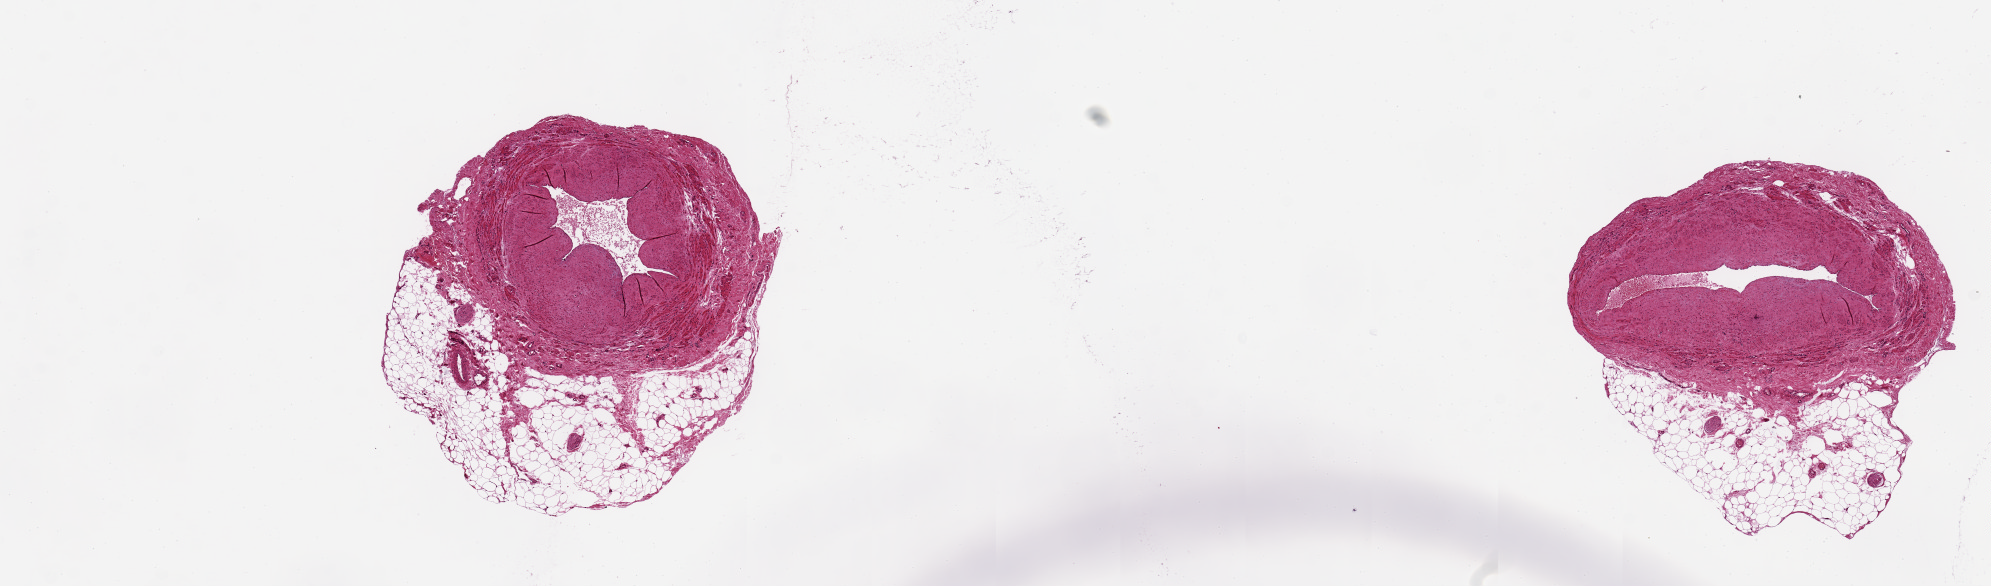
Whole-slide image, H&E stain — a low-resolution overview of the entire scanned area, about 15.8 x 4.6 mm (from a 20x scan), PAXgene-fixed, paraffin-embedded tissue, section of tibial artery (target tissue), donor tissue sample. Donor: male.
- reviewer comment on this tissue sample: 2 pieces, 3x2 mm; 80% atheromatous intimal narrowing